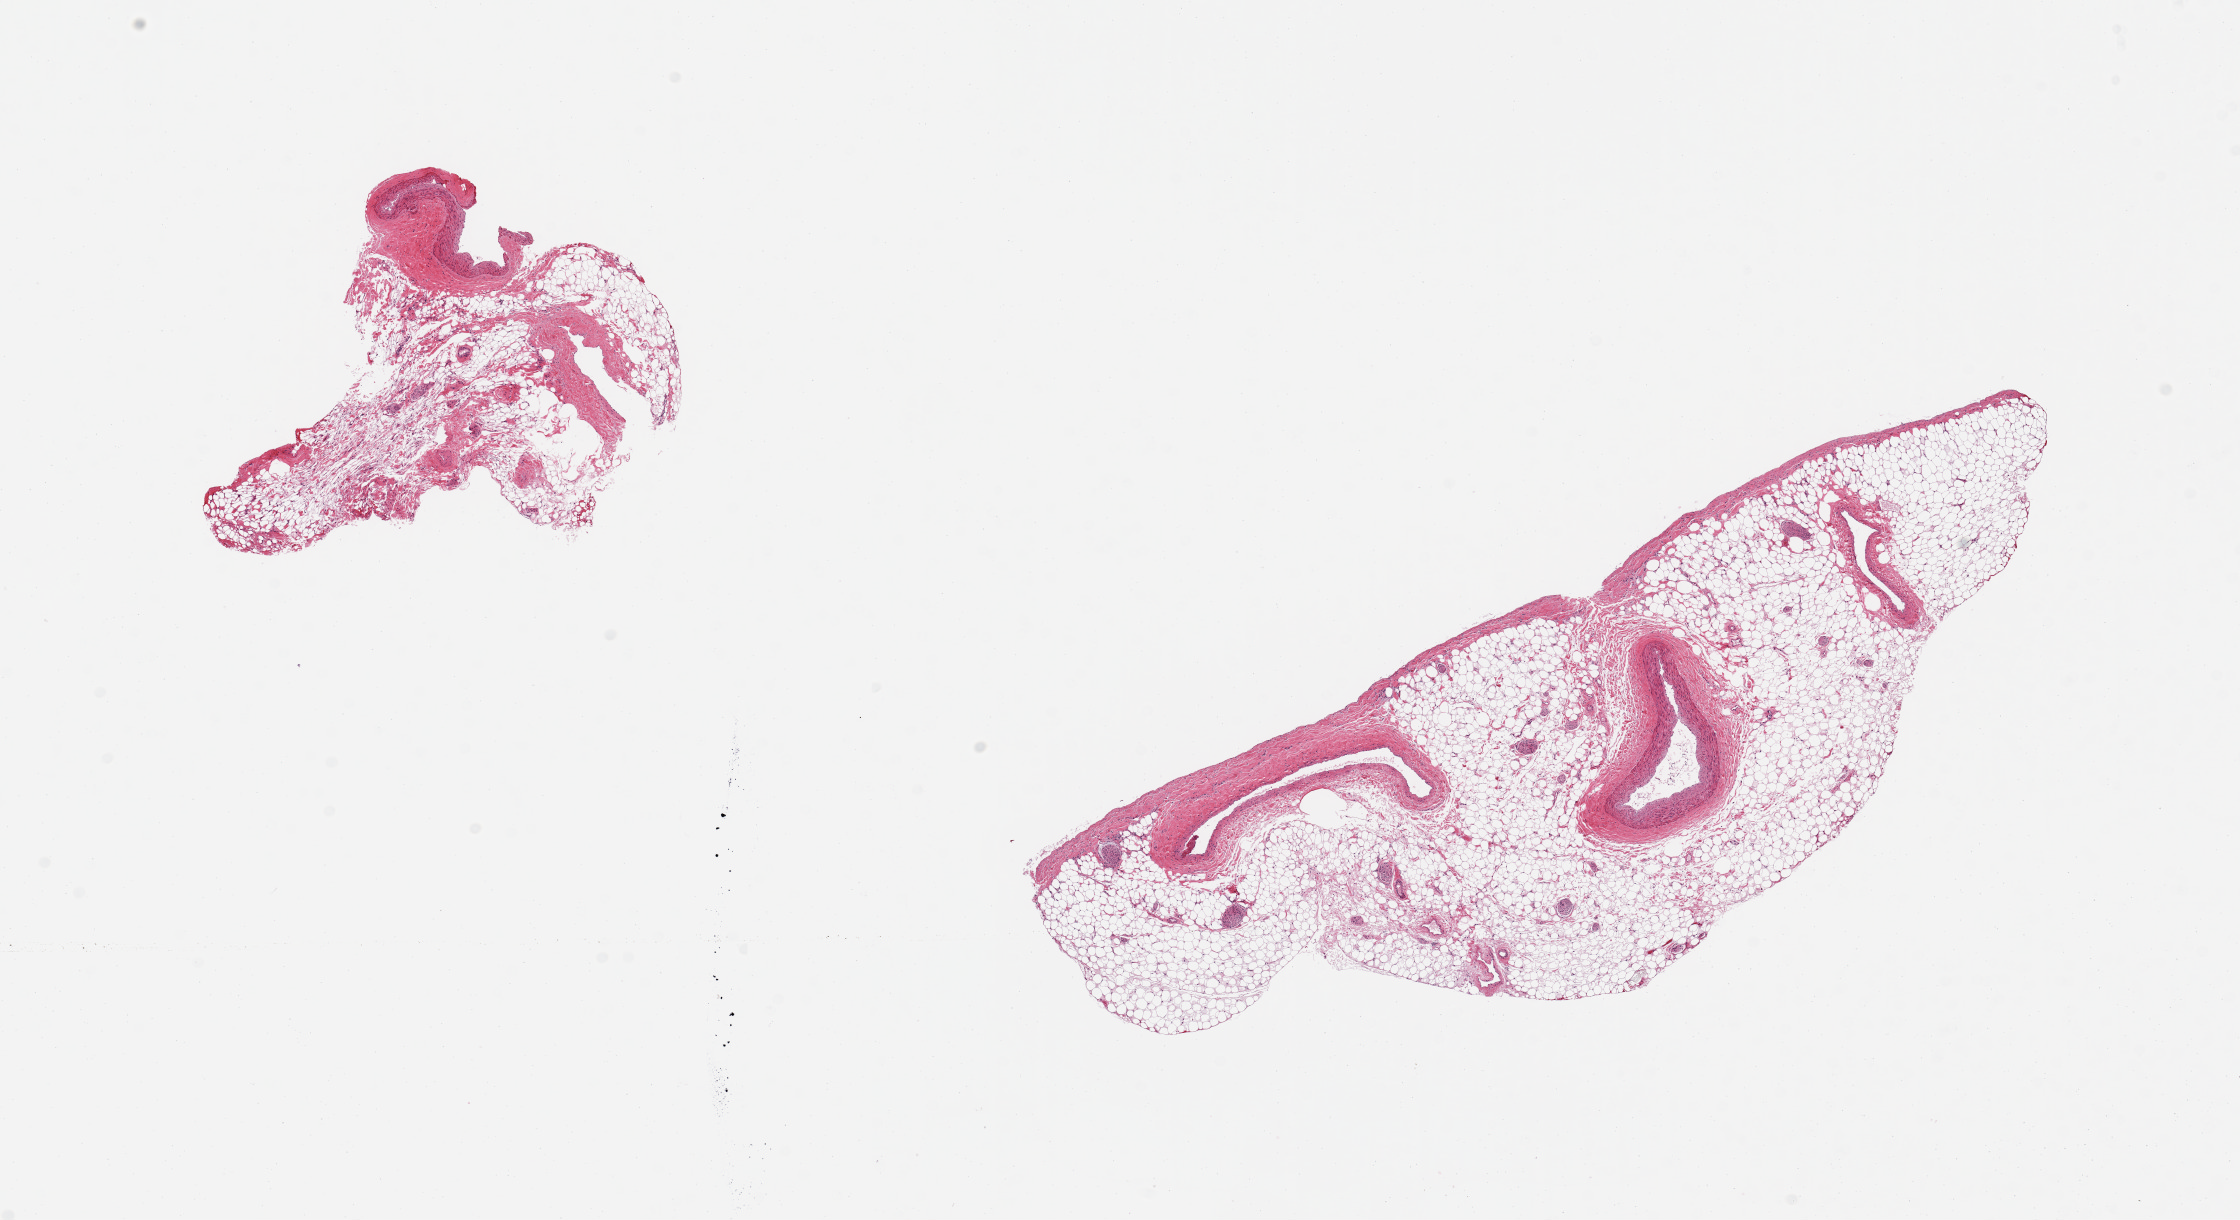
Whole-slide image, haematoxylin and eosin stain, shown as a low-resolution overview of the whole scanned area (about 17.7 x 9.7 mm). PAXgene-fixed paraffin-embedded (PFPE) section. Section of coronary artery (target tissue). Tissue donor sample. Male donor.
Review note (as recorded): 2 pieces, coronary branch twigs, not main coronary artery, mainly epicardial fat.